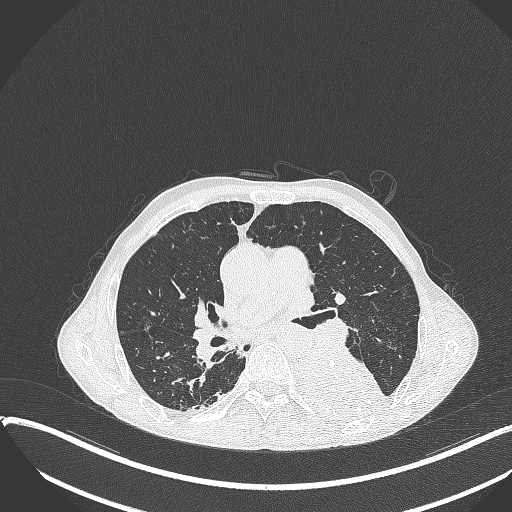
Chest CT, one axial slice; slice 214 of 401 in the series (ordered by position); reconstruction kernel B70f; 120 kVp; lung window (W 1500 / L -600 HU); 1 mm slice thickness; 512 × 512 image matrix, field of view 400 × 400 mm. Male patient, age 57 years. Case-level facts recorded for this patient, not image findings: clinical TNM (as recorded): T4 N0 M0.
Structures marked on this image (bounding box drawn by a radiologist):
- lung tumour (recorded histology: squamous cell carcinoma): box from (x=290, y=348) to (x=394, y=425) px